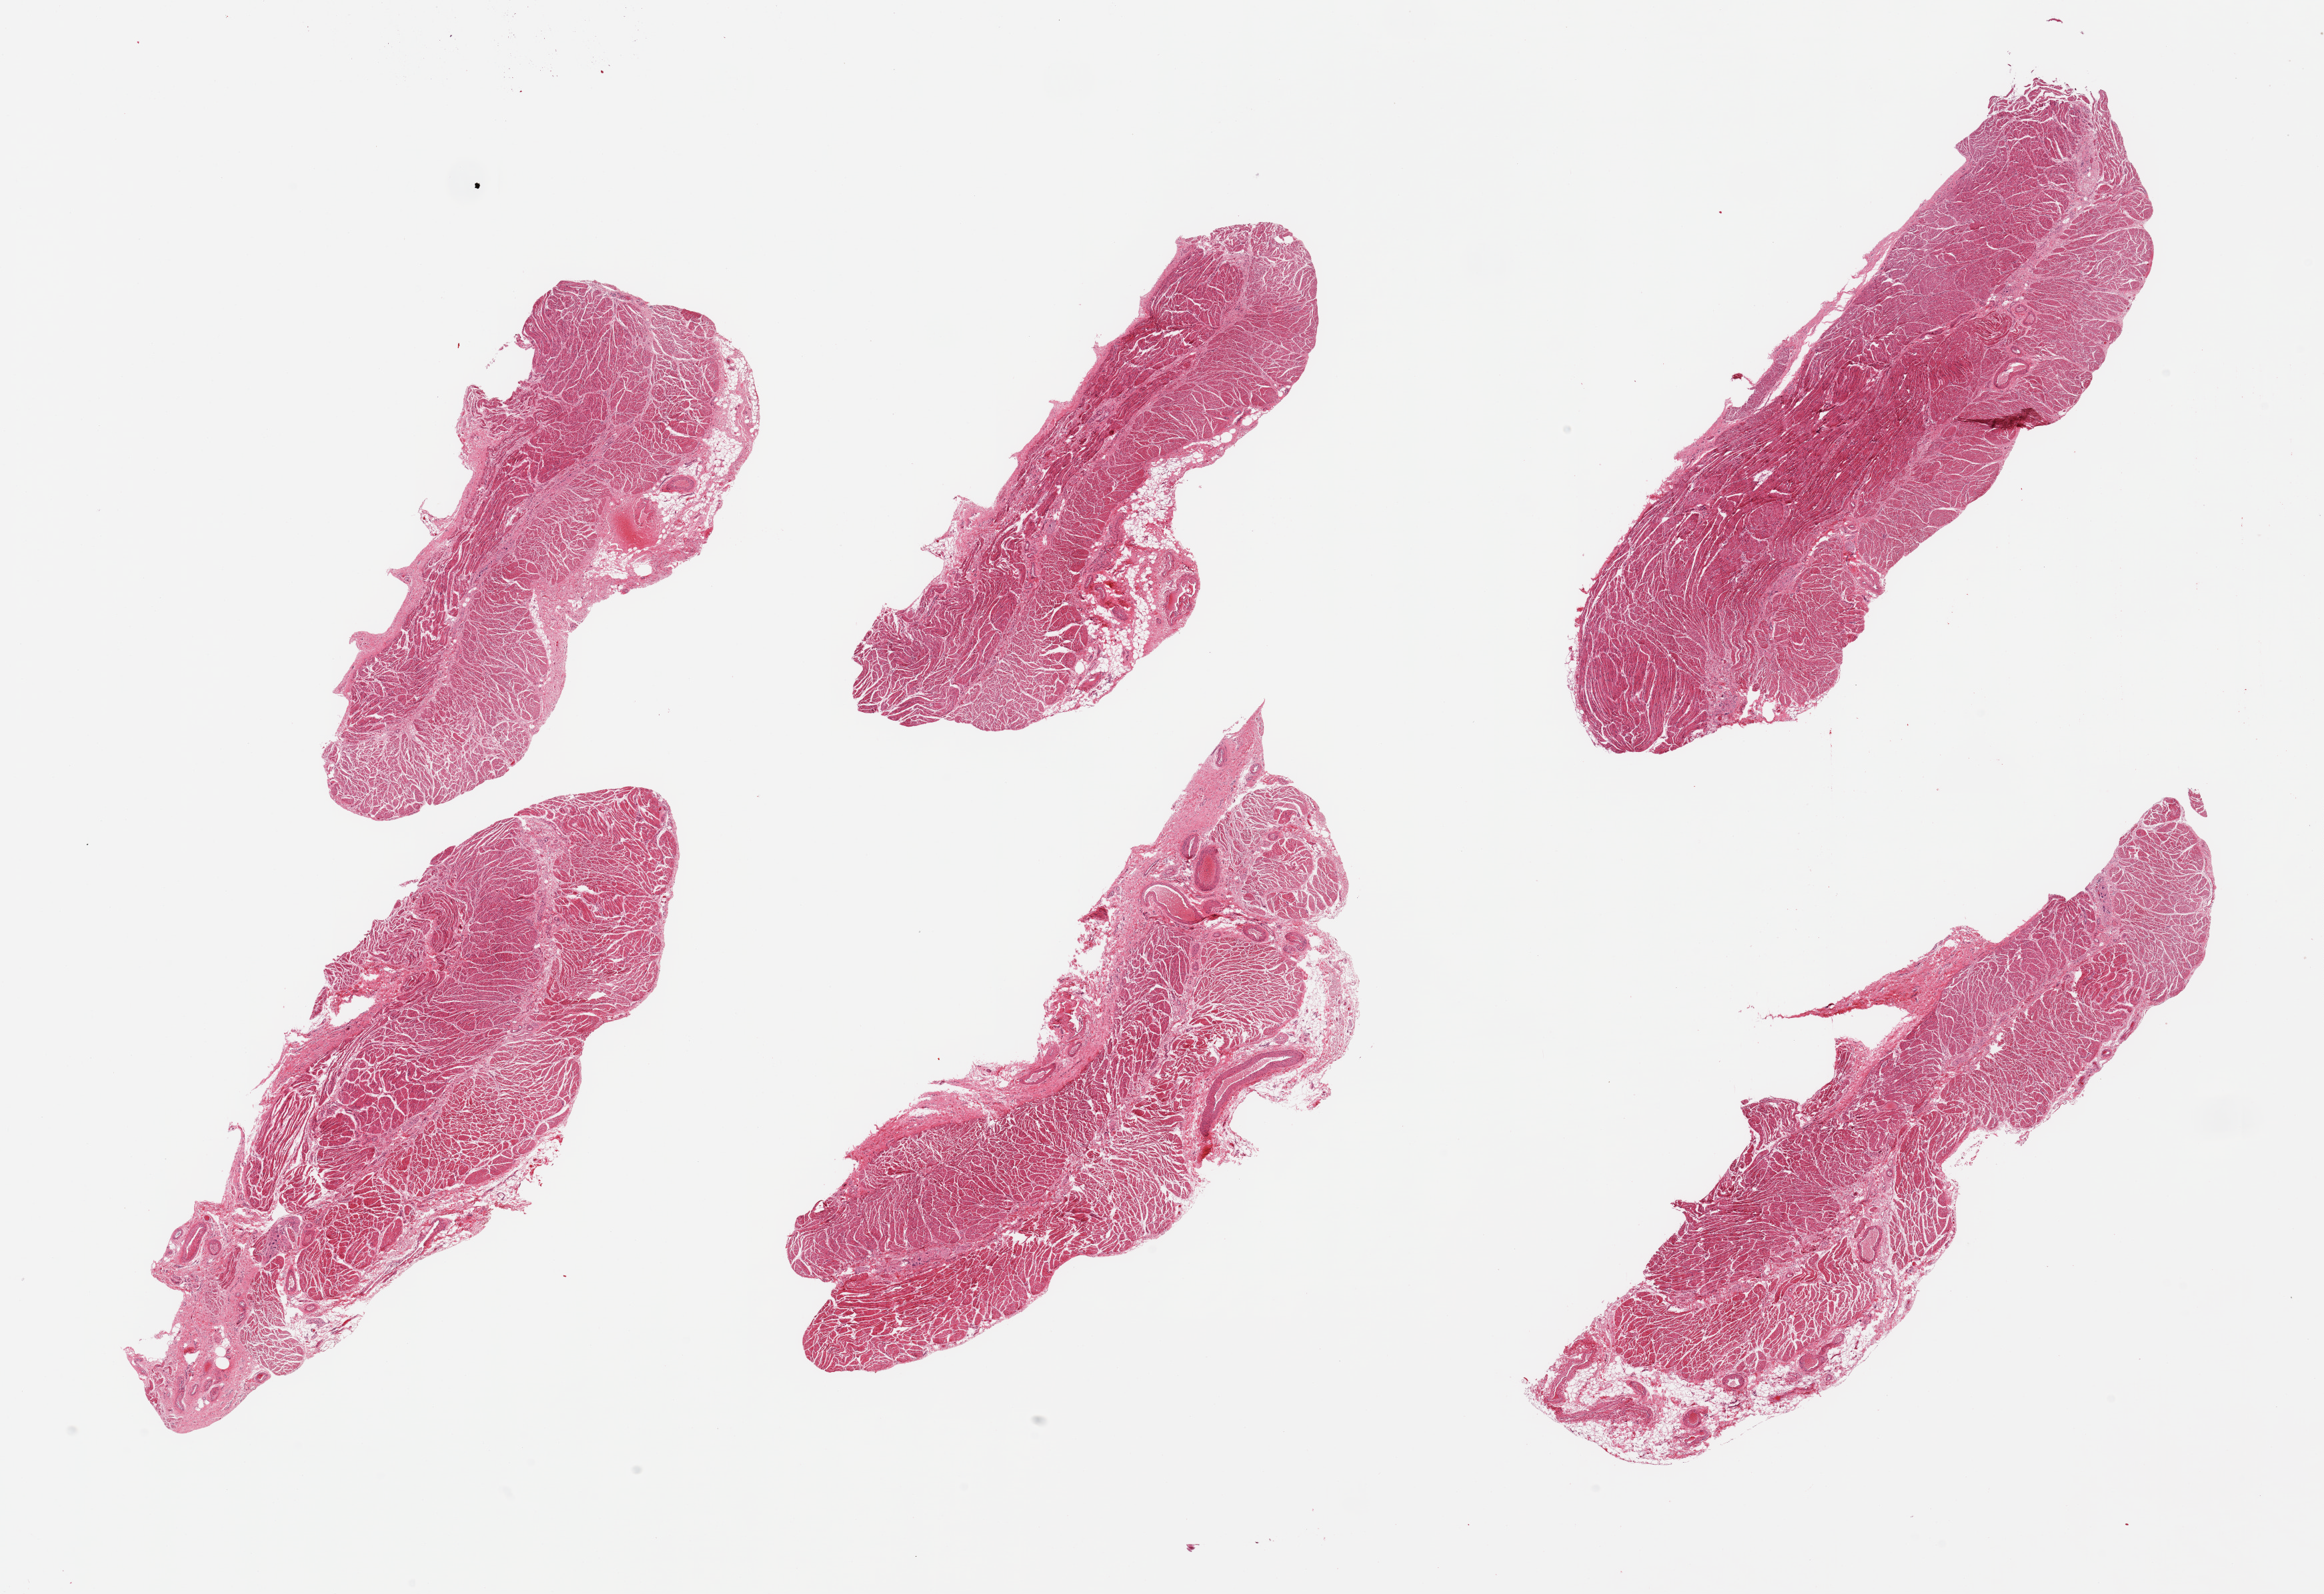
Digitized haematoxylin and eosin-stained section, whole scanned area (about 27.6 x 18.9 mm) shown as a low-resolution overview, PAXgene-fixed, paraffin-embedded tissue, target tissue: gastroesophageal junction, tissue donor sample. Male donor.
- pathologist's review note for this sample: 6 pieces; target muscularis, few pieces with small amount of attached fat/vessels